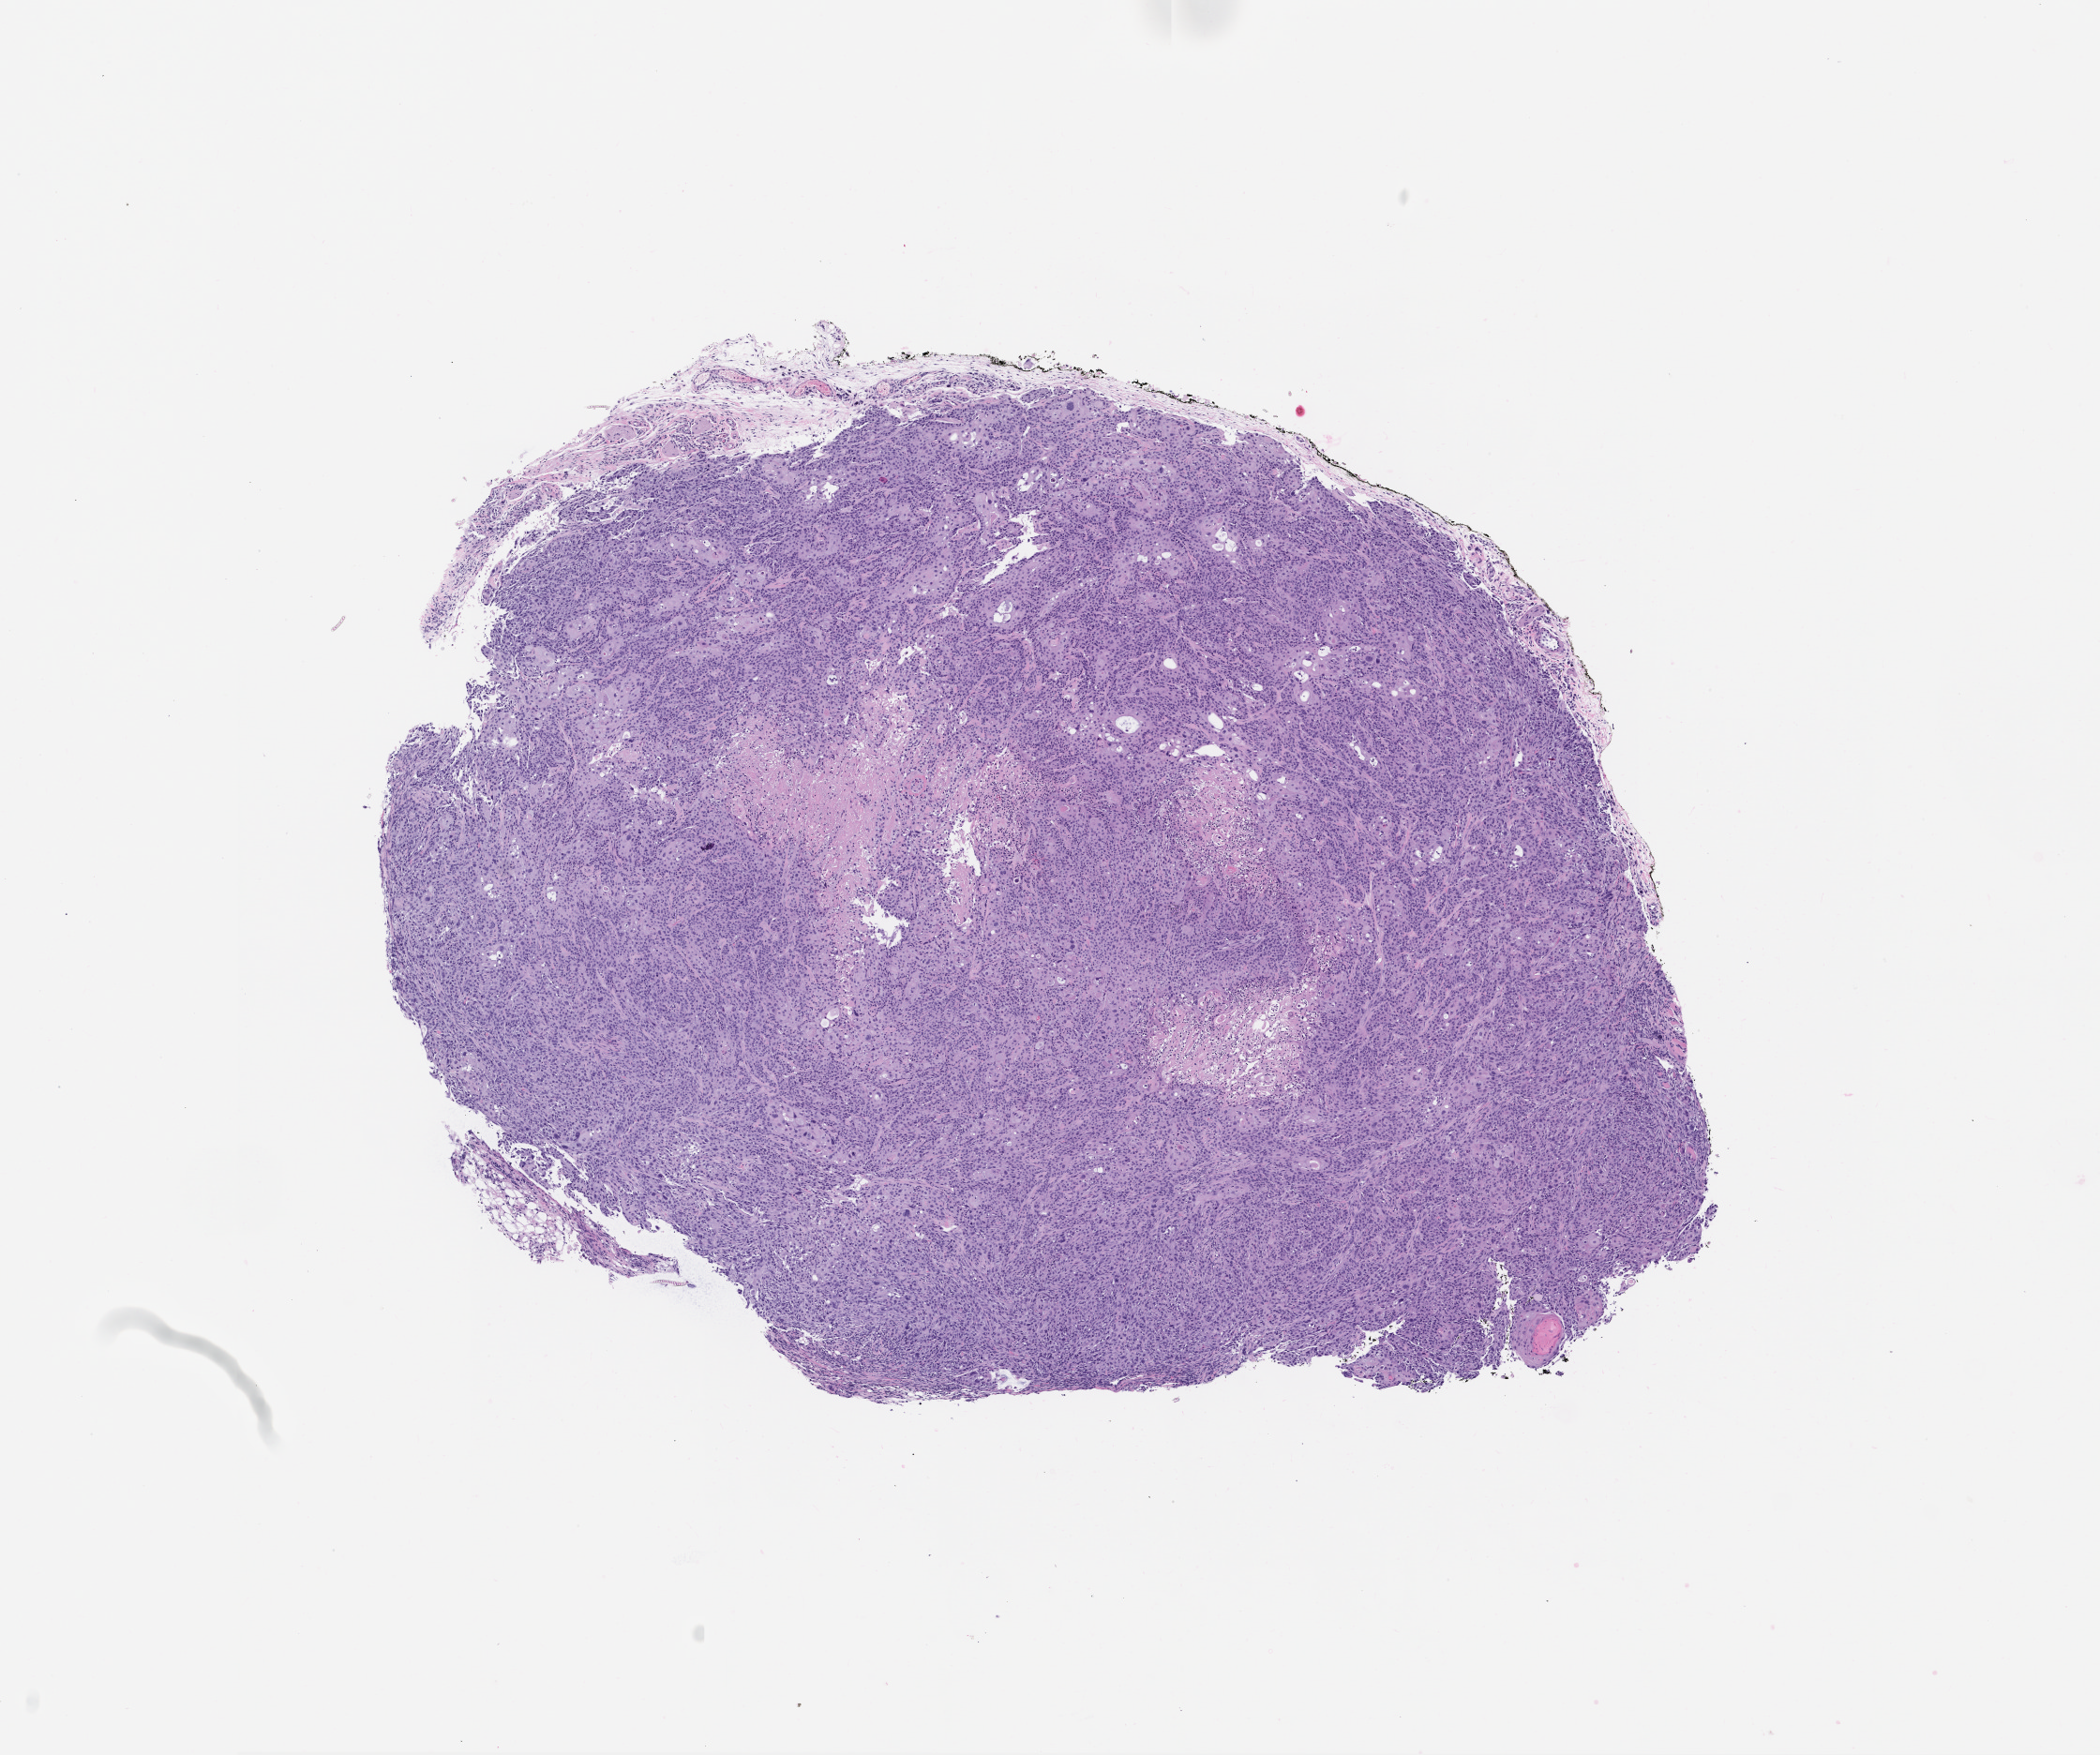
Whole-slide image, hematoxylin and eosin (H&E): patient-derived xenograft (human tumor grown in a mouse), passage 0 — whole scanned area (about 9.0 x 7.5 mm) shown as a low-resolution overview, formalin-fixed, paraffin-embedded (FFPE) tissue, tumor site category: head and neck.
- originating patient diagnosis: Mucoepidermoid Carcinoma